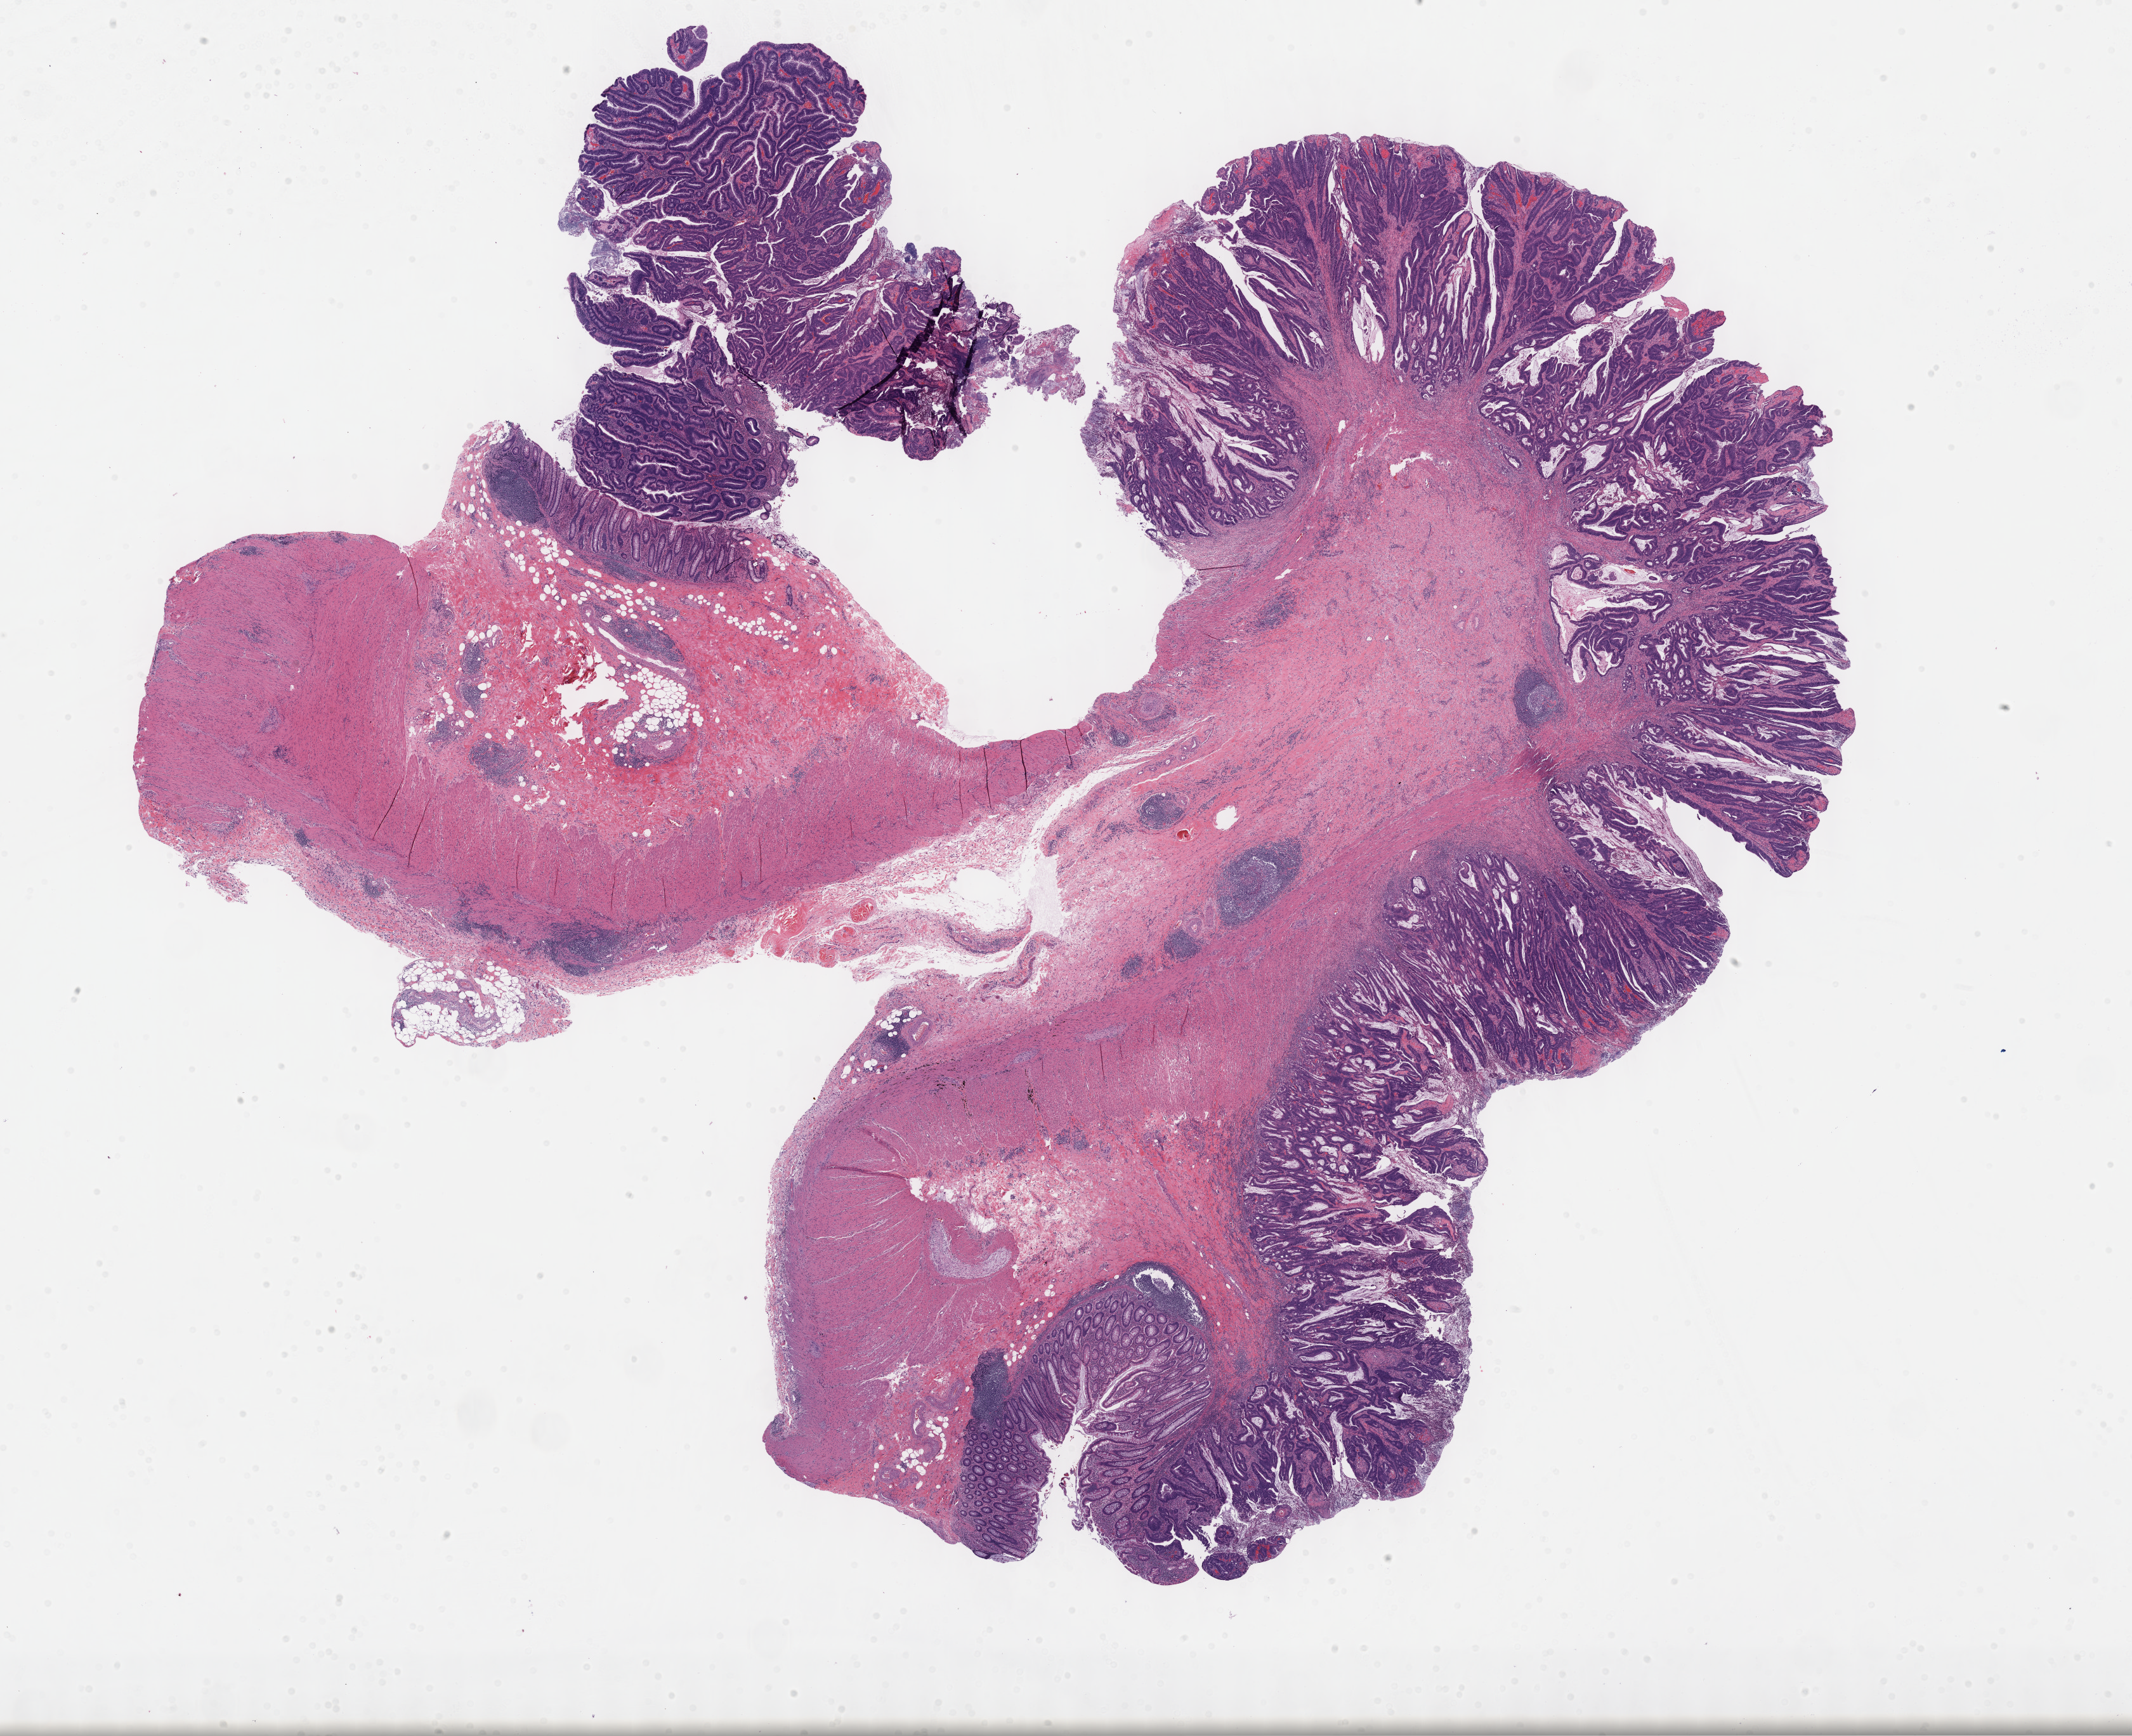
Digitized H&E tissue section (whole slide) — a low-resolution overview of the entire scanned area, about 27.2 x 22.1 mm (acquisition: 40x scan). Formalin-fixed paraffin-embedded (FFPE) diagnostic section. Colon, primary tumour sample. Patient: male, age at initial diagnosis 61 years.
TNM: T2 N0 M0. Diagnosis: Adenocarcinoma, NOS (cecum). AJCC pathologic stage: I (7th edition). Lymph nodes positive (case pathology): 0 of 23 examined.